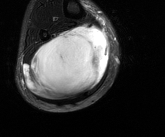
MRI of an extremity soft-tissue mass, one axial slice; slice 59 of 81 in the series (ordered by position); T2-weighted fat-saturated; MR volume resampled by the dataset authors to the PET/CT grid (not the native acquisition matrix); 3.27 mm slice thickness; 165 × 137 image matrix, field of view 161 × 134 mm. Male patient. Case-level facts recorded for this patient, not image findings: histological type: liposarcoma - round cell; grade: high; site of the primary tumour: right calf.
Outlined on this slice (expert contour drawn on MRI and transferred to this co-registered scan by the dataset authors):
- gross tumour volume (mass): bounding box <23,23,109,101> (left, top, right, bottom; pixels)